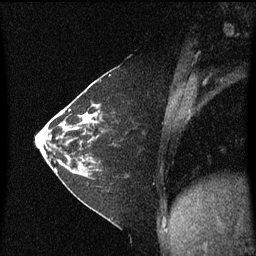
Breast MRI (dynamic contrast-enhanced), one sagittal slice. Slice 25 of 60 in the series (ordered by position). Dynamic contrast-enhanced series, image 2 of 3 at this slice position (ordered by acquisition). 1.5 T. TE 4.2 ms, TR 8.4 ms. 2 mm slice thickness. 256 × 256 image matrix, field of view 200 × 200 mm. Patient: female, 36 years. From the clinical record (not read from this slice): setting: breast cancer imaged before/during neoadjuvant chemotherapy; receptor status: HR-positive, HER2-negative.
Outlined on this slice (semi-automatically segmented with operator editing):
- analysis volume of interest (the breast-tissue region the enhancement analysis was run in; not a lesion): bounding box <66,102,104,179> (left, top, right, bottom; pixels)
- tumour enhancement mask (voxels above the 70 % enhancement threshold inside the analysis volume of interest): <66,114,98,129>